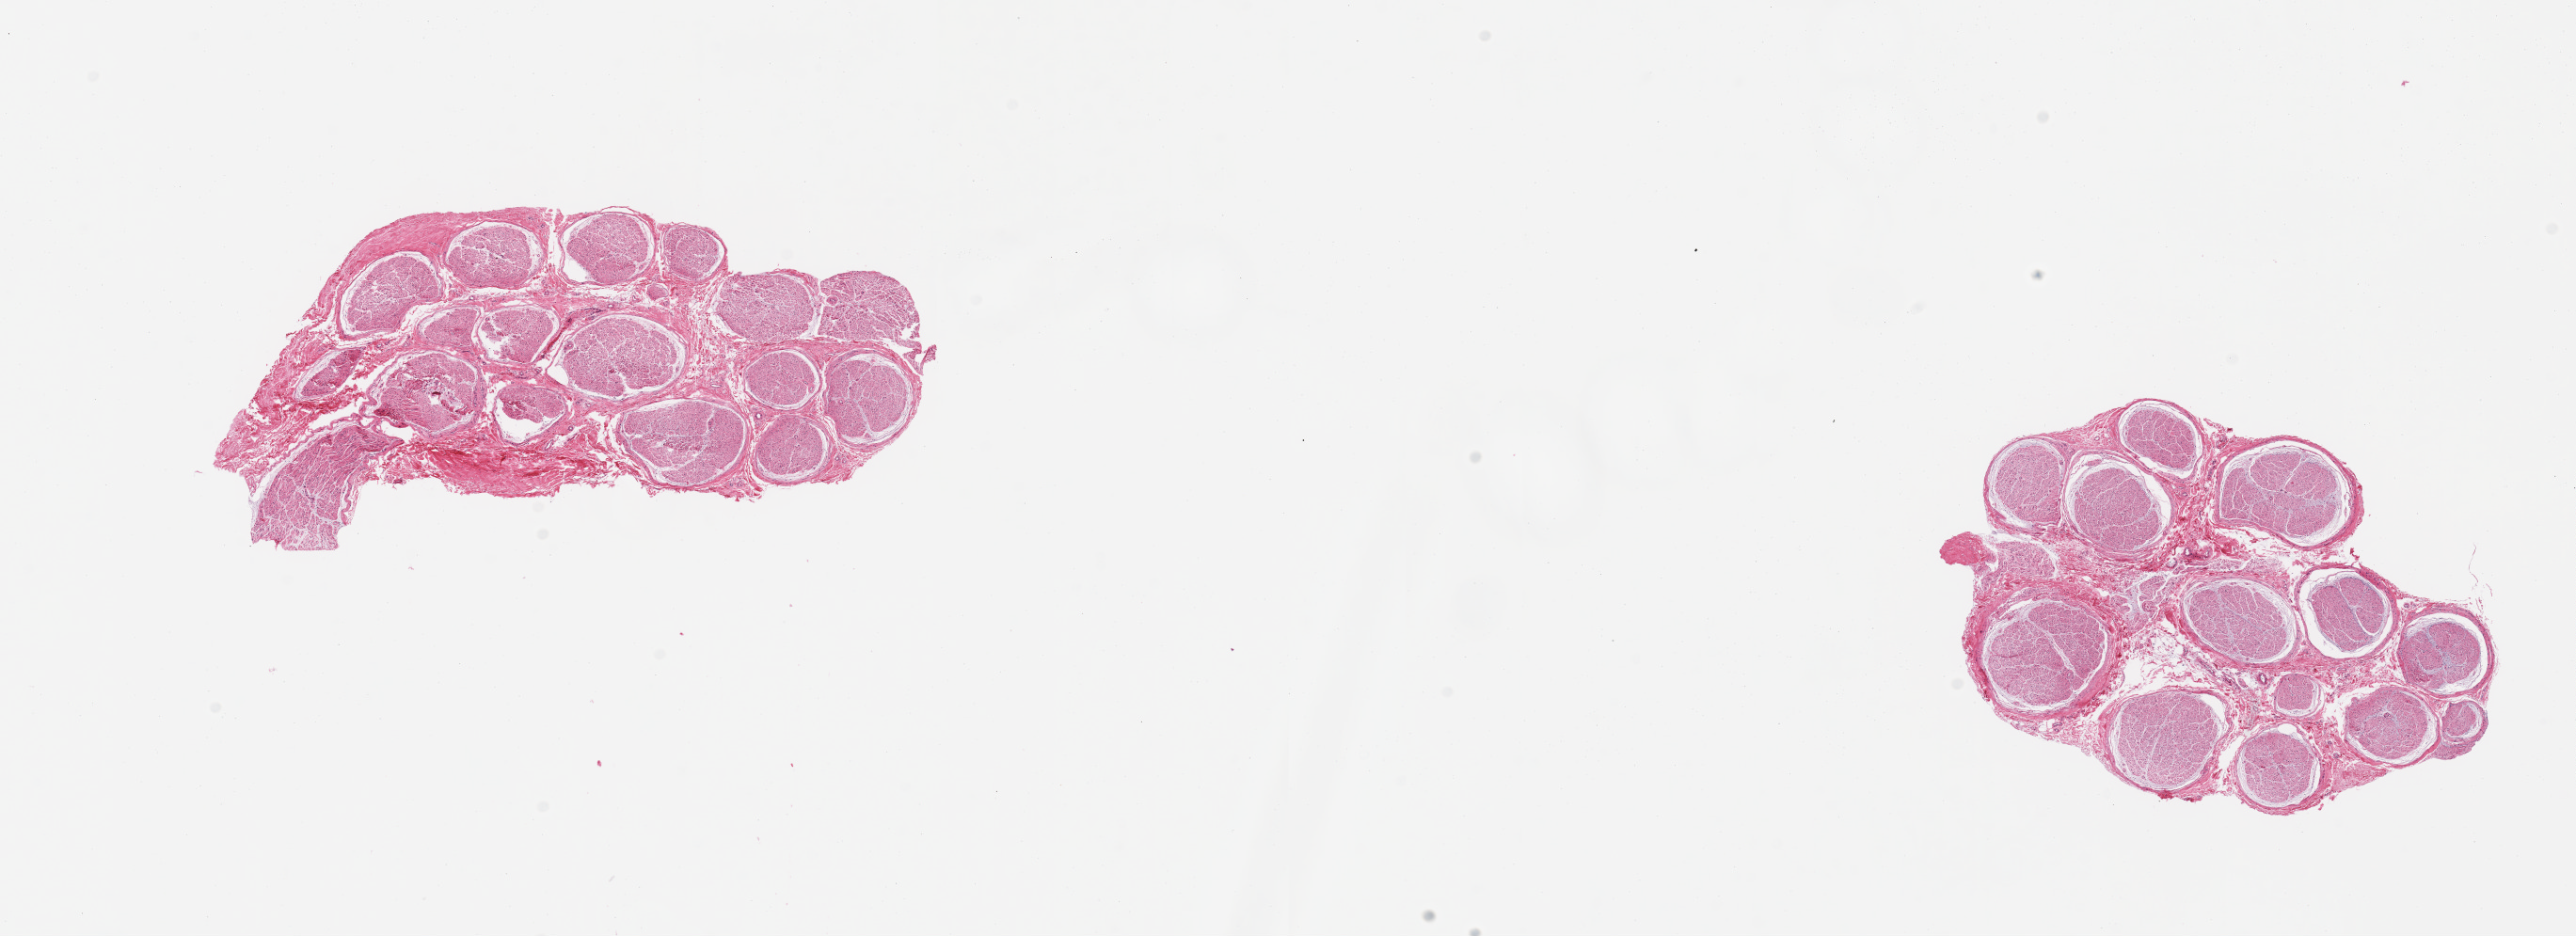
Hematoxylin and eosin (H&E) whole-slide image — a low-resolution overview of the entire scanned area, about 21.7 x 7.9 mm (slide scanned at 20x). PAXgene-fixed, paraffin-embedded tissue. Target tissue: tibial nerve. Donor tissue sample. Donor: male.
Review note (as recorded): 2 pieces; small amounts of internal fat.